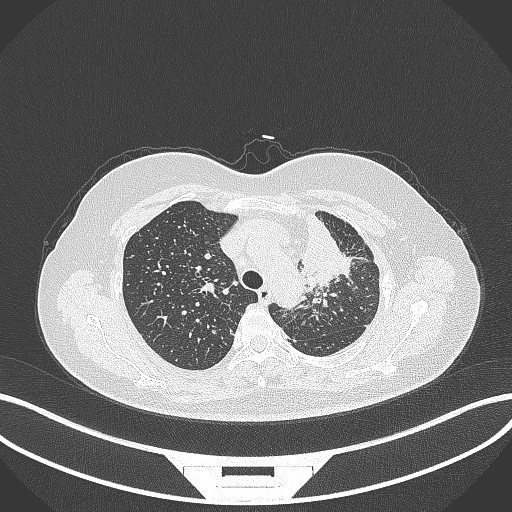
Chest CT, one axial slice; reconstruction kernel B70f; 120 kVp; lung window (W 1500 / L -600 HU); 1 mm slice thickness; 512 × 512 image matrix, field of view 400 × 400 mm. Patient: female, 49 years. Case-level facts recorded for this patient, not image findings: clinical TNM (as recorded): T1c N0 M1.
Annotated regions visible in this slice (rectangle marked by the reading radiologist):
- lung tumour (recorded histology: adenocarcinoma): bounding box [x1, y1, x2, y2] px = [294, 209, 356, 289]